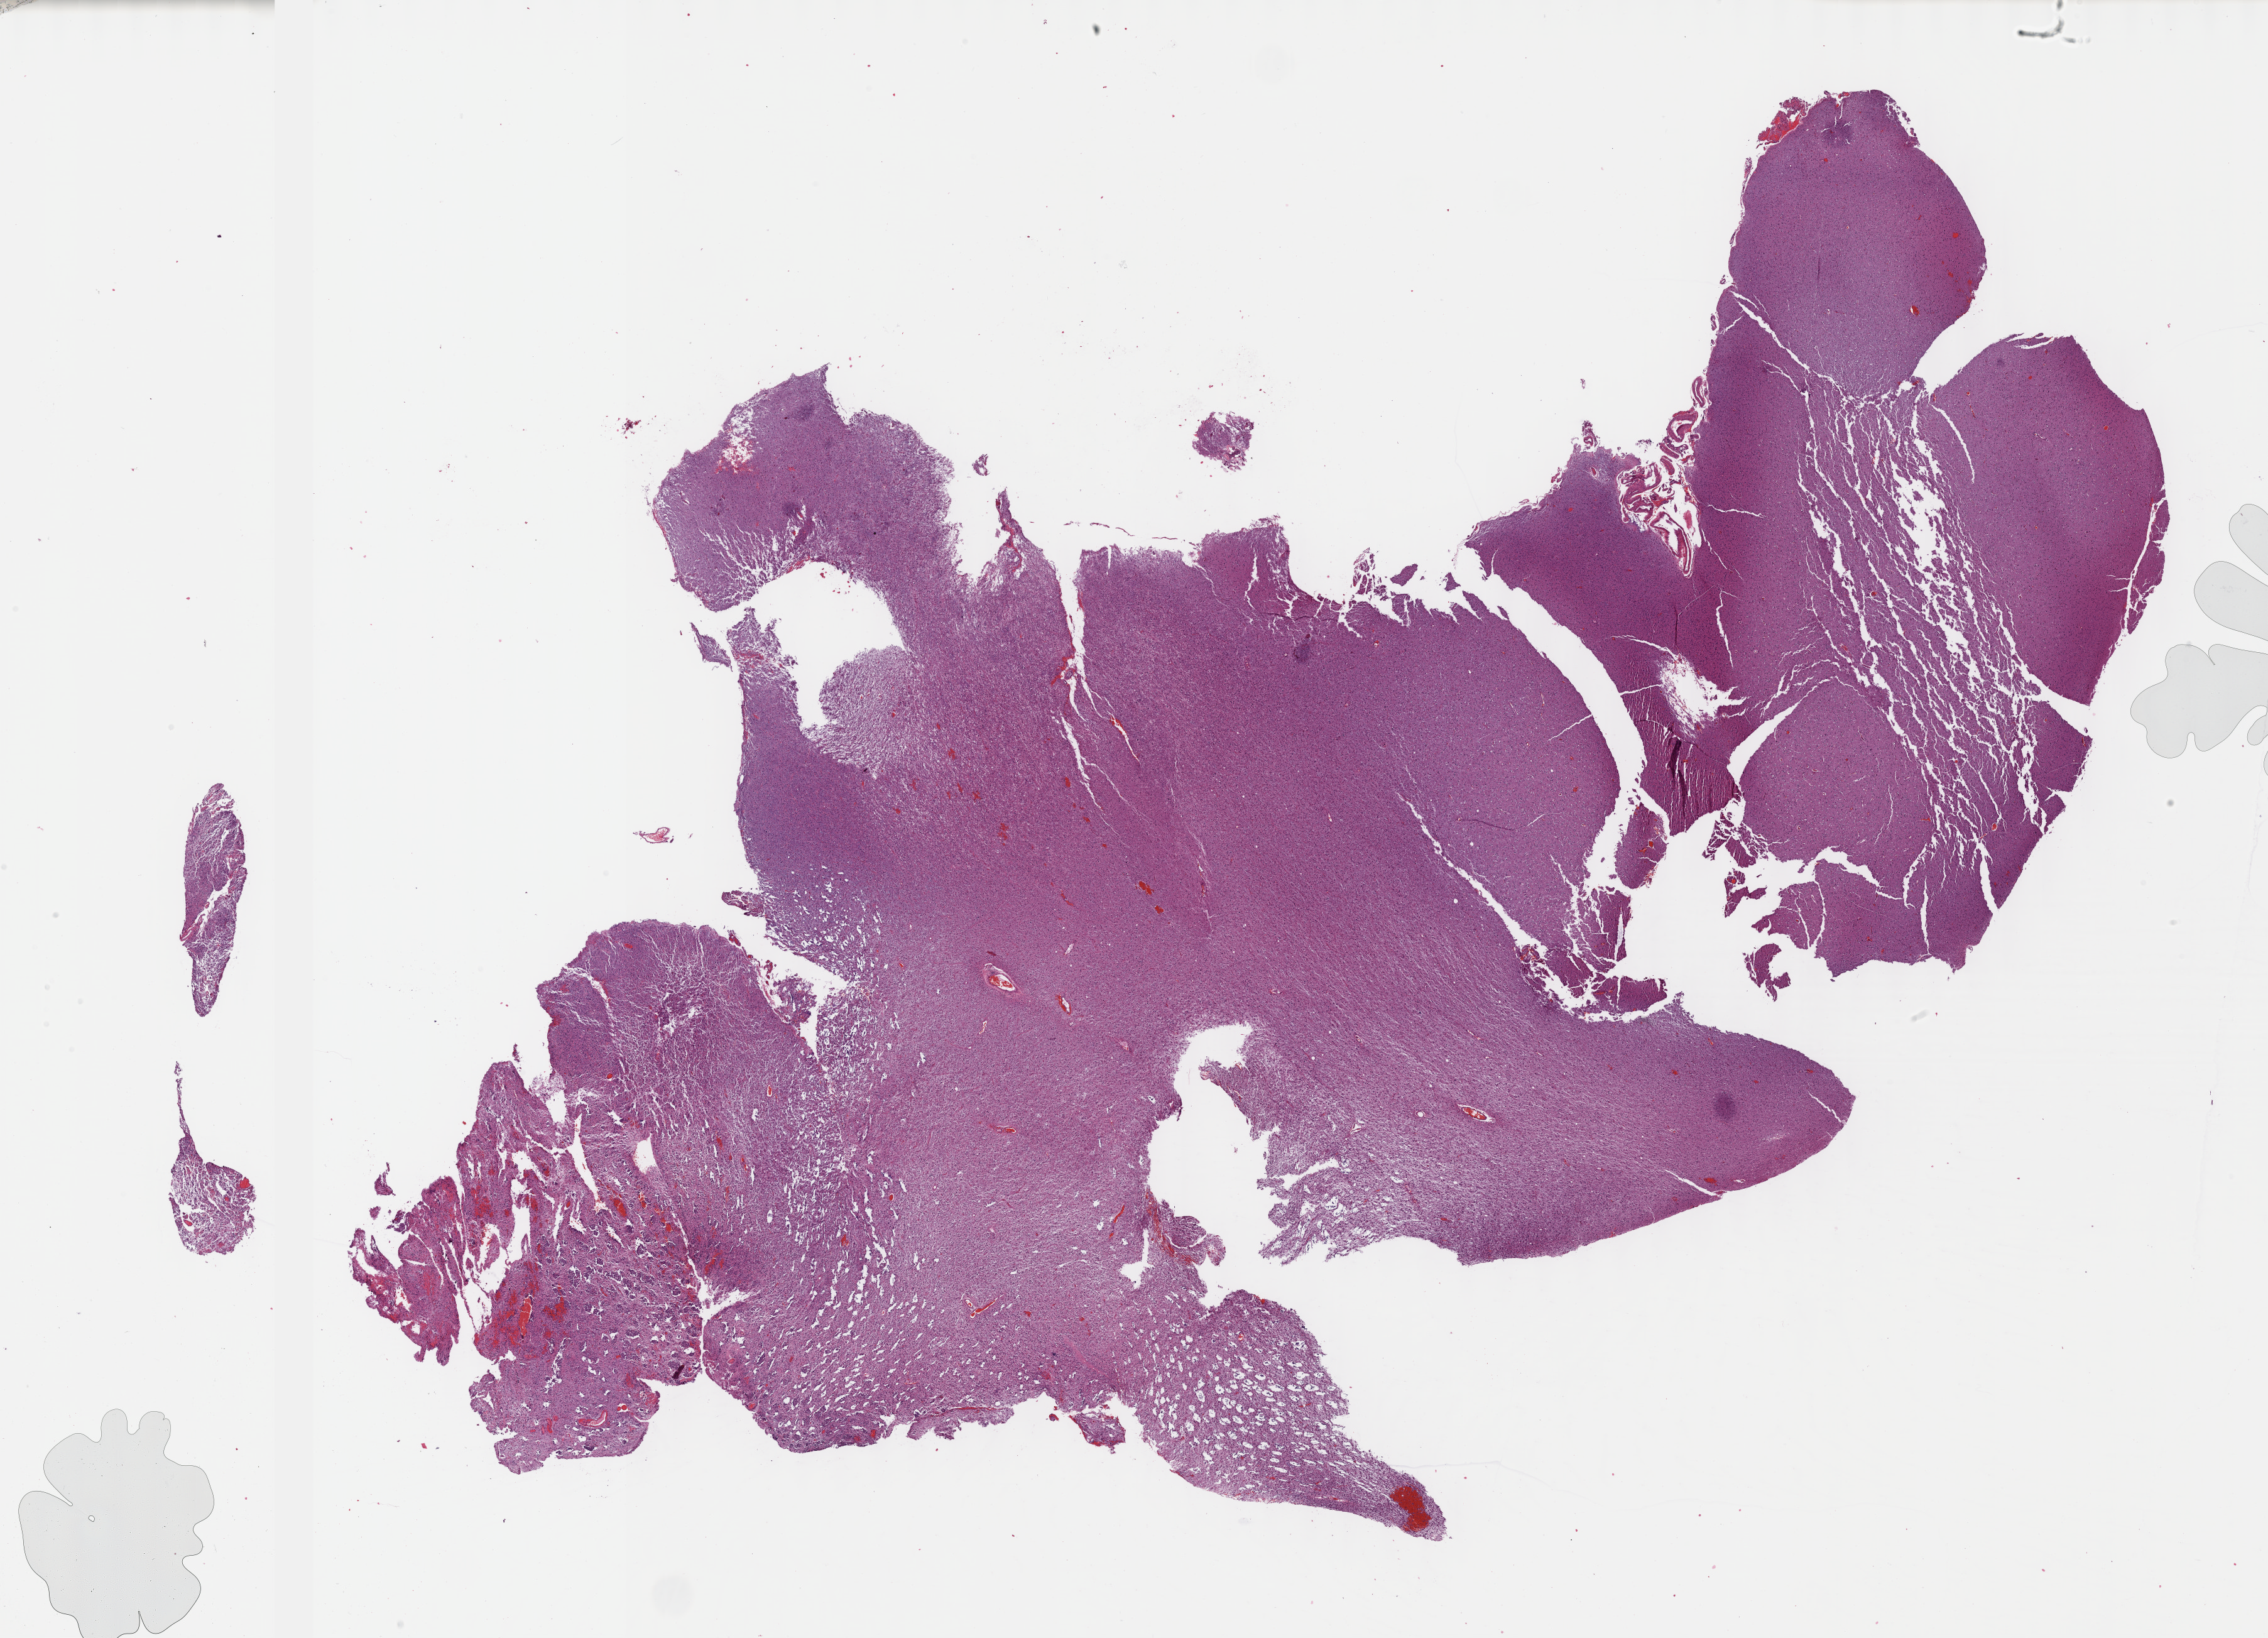
Digitized Hematoxylin and eosin (H&E) stained tissue section (whole slide), whole scanned area (about 29.2 x 21.1 mm, acquisition: 40x scan) shown as a low-resolution overview. Formalin-fixed paraffin-embedded (FFPE) diagnostic section. Sample: primary tumour, brain. Patient: male, age at initial diagnosis 28 years. Histologic grade: G2 (moderately differentiated).
Laterality: right. Pathologic diagnosis: Astrocytoma, NOS (cerebrum).